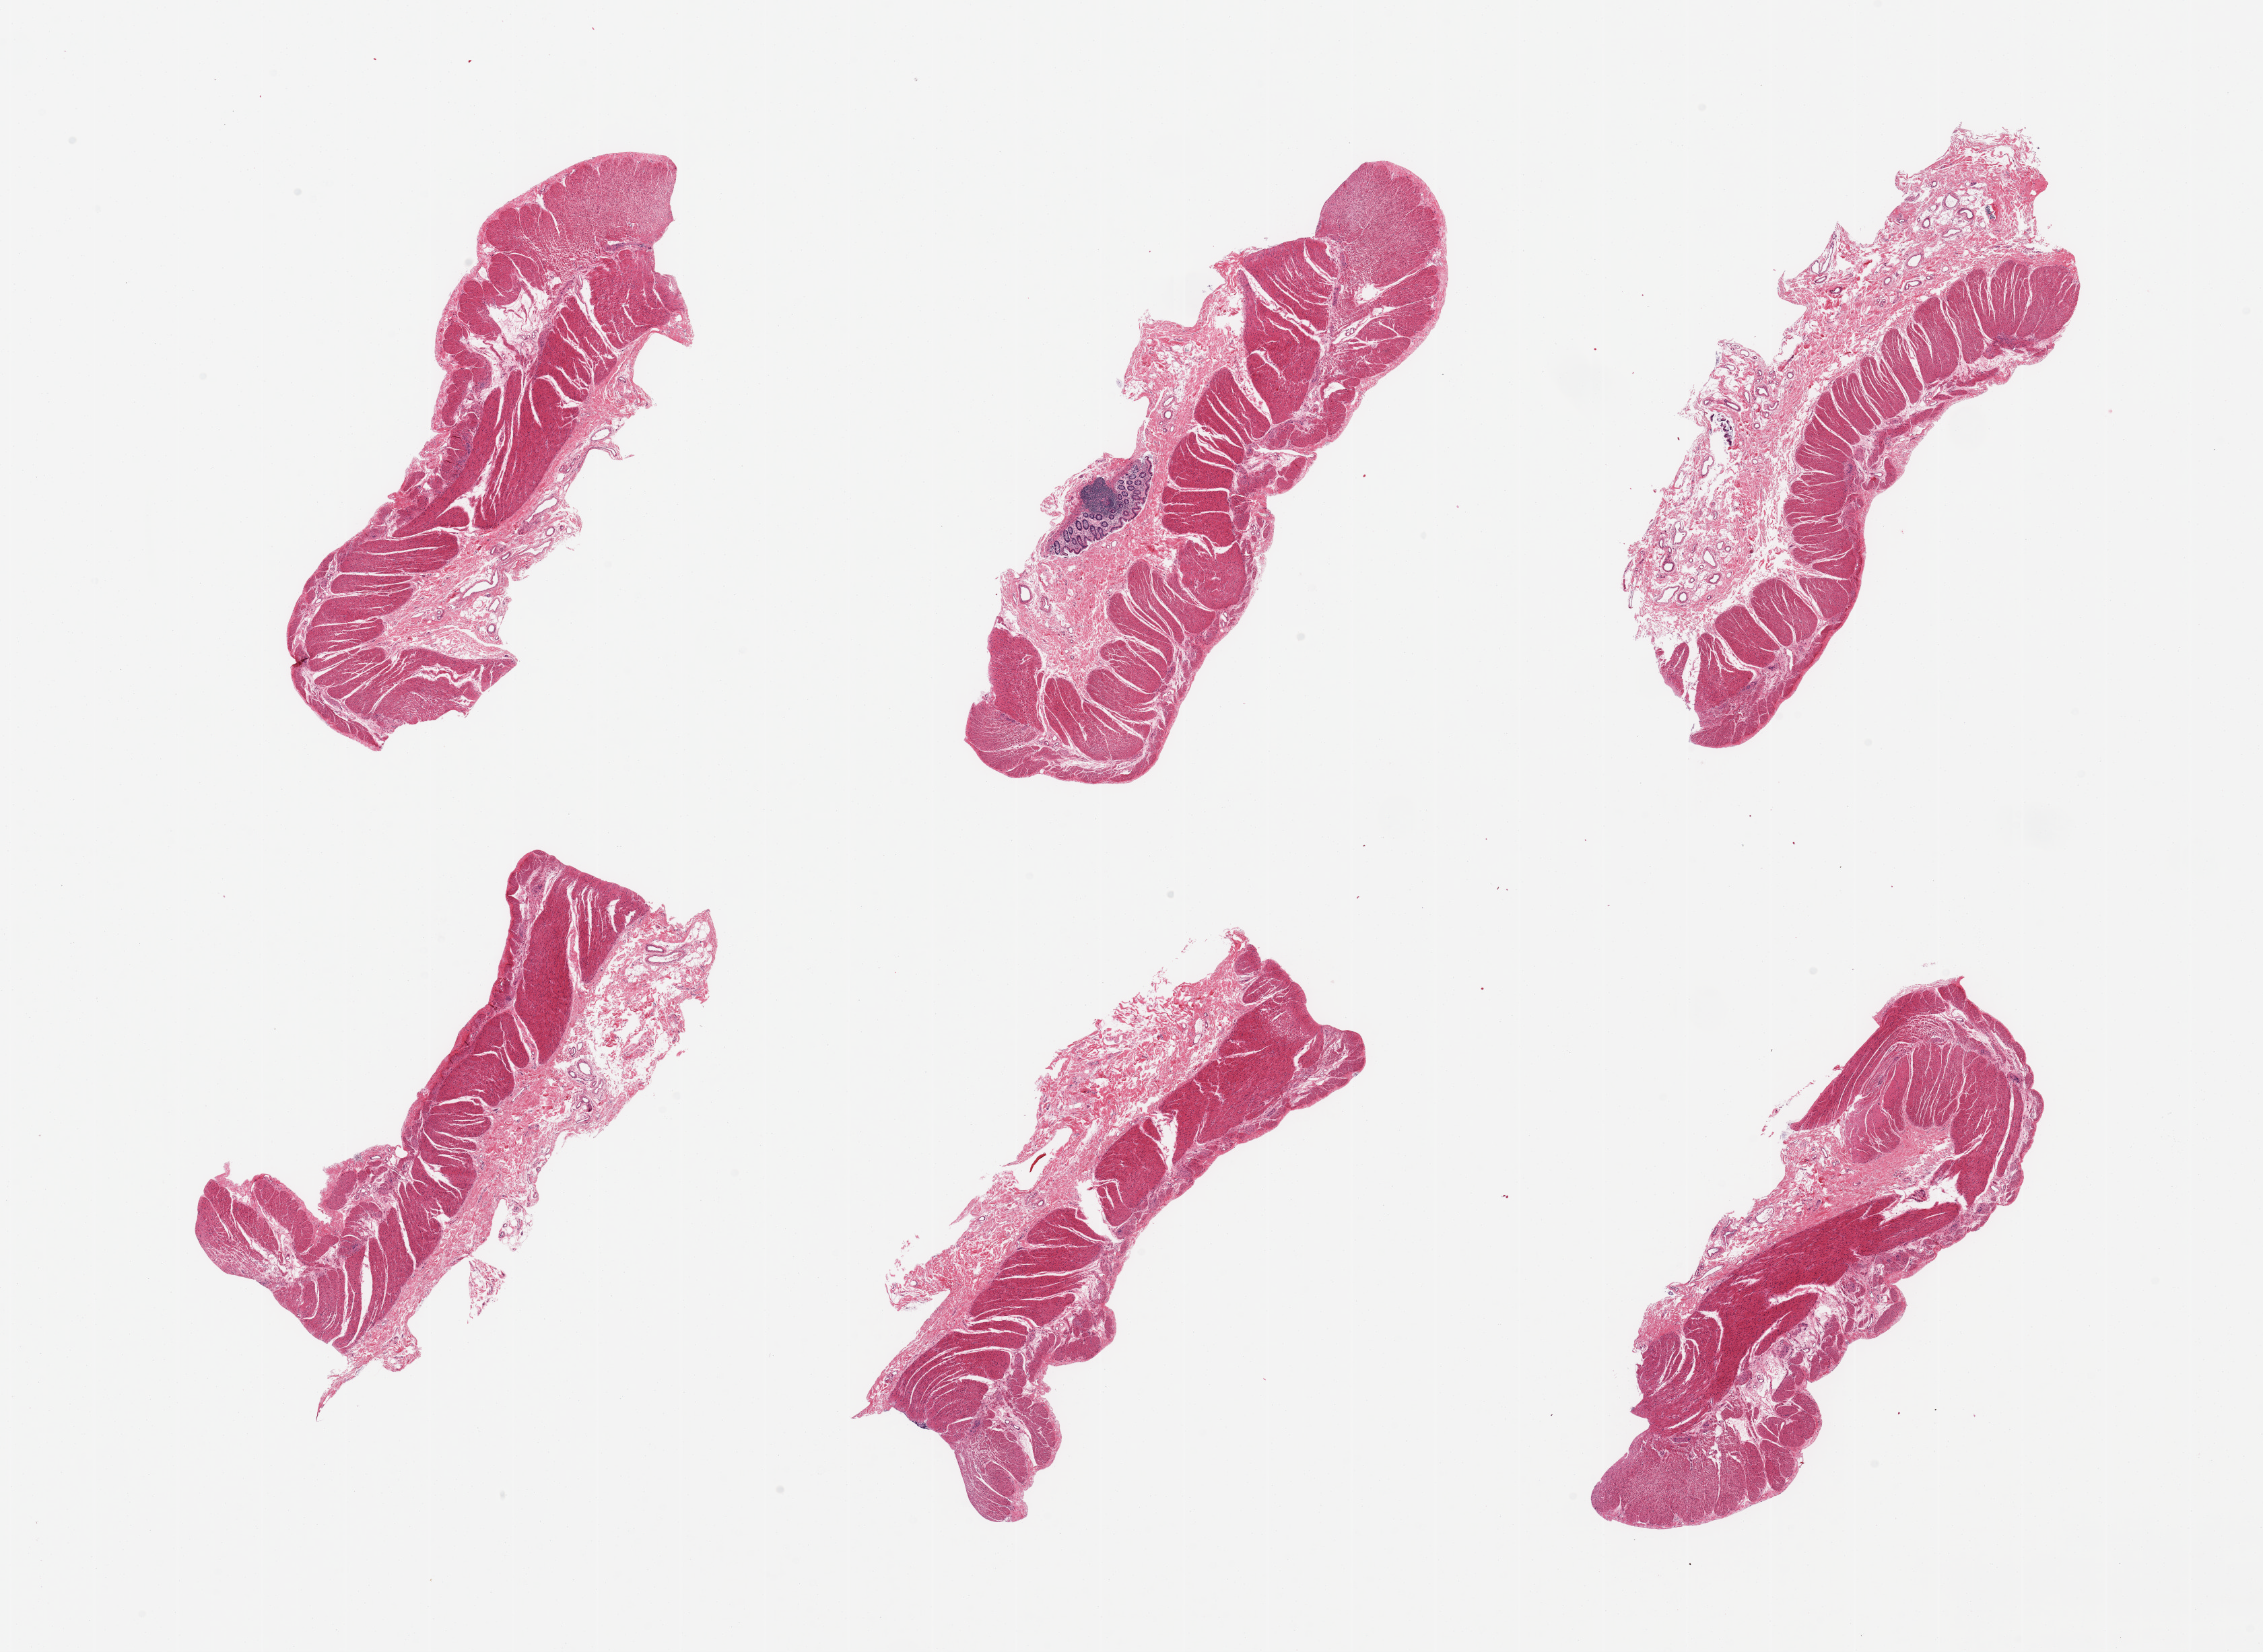
Digitized haematoxylin and eosin-stained section, brightfield, whole scanned area (about 26.6 x 19.4 mm) shown as a low-resolution overview. PAXgene-fixed paraffin-embedded (PFPE) section. Section of sigmoid colon (target tissue). Tissue donor sample.
Review note (as recorded): all with abundant submucosal stroma up to 1.6mm thick.